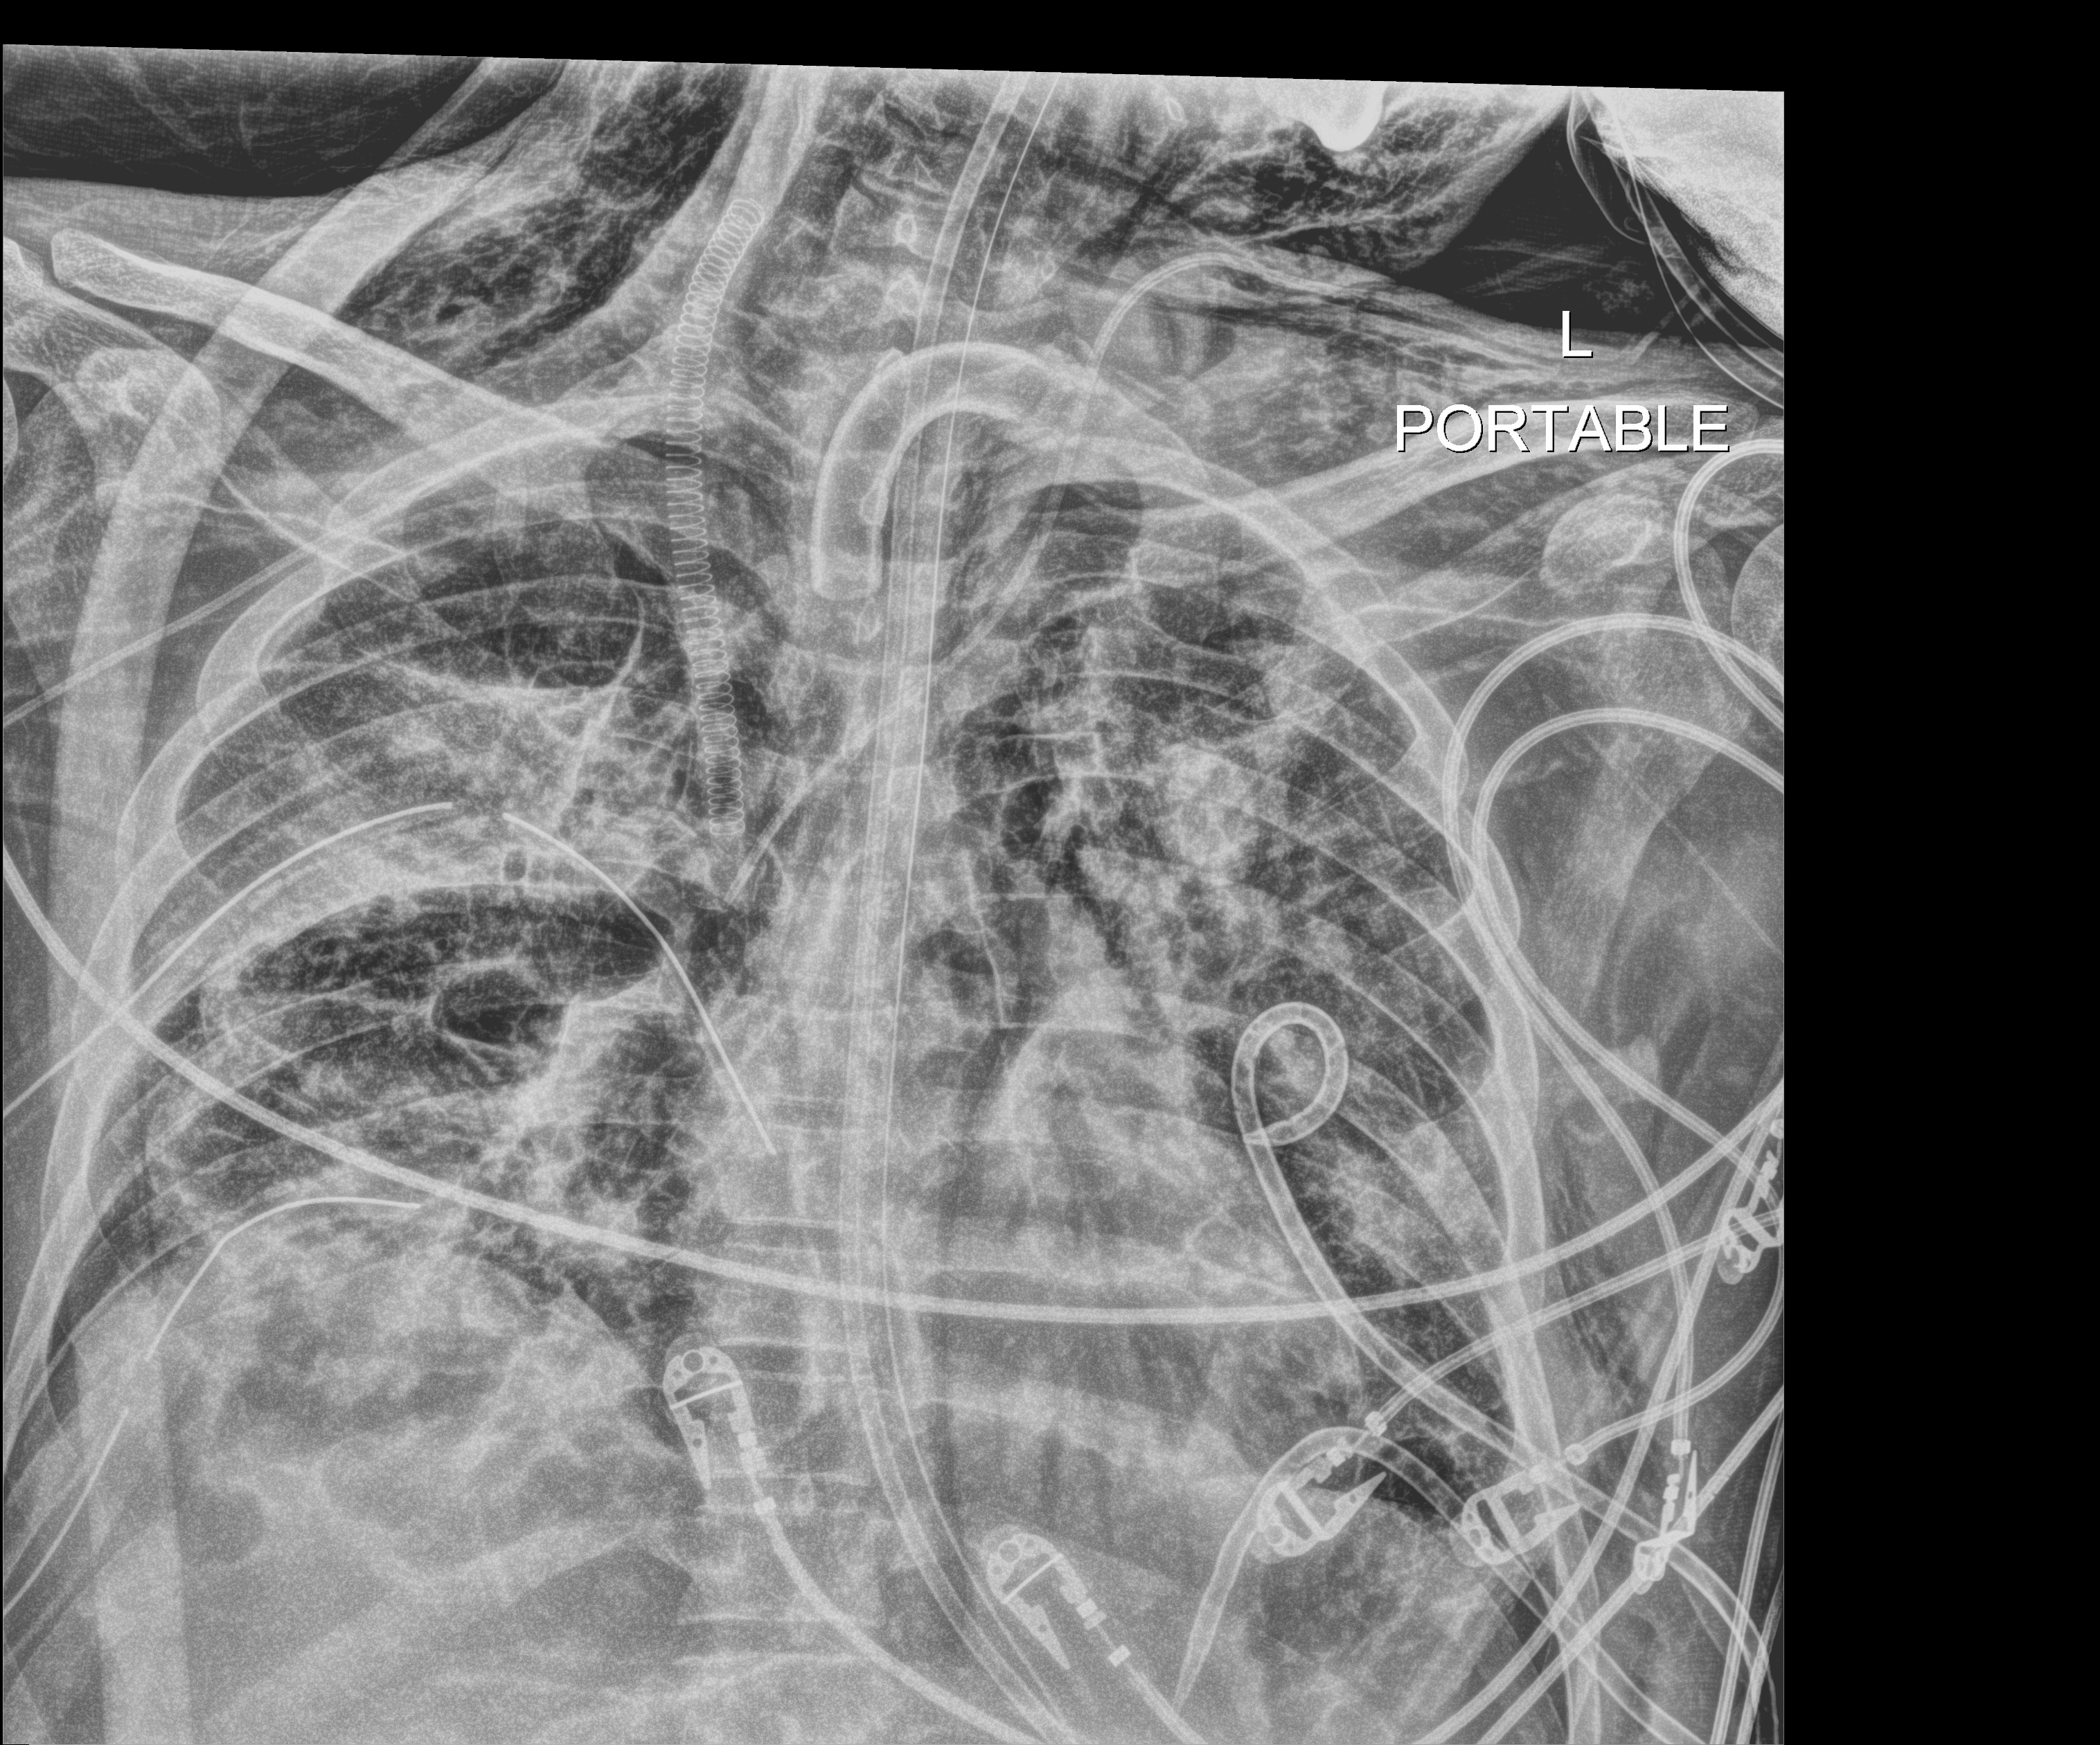
Chest X-ray; anteroposterior (AP) projection. Patient hospitalised with COVID-19, aged 18–59 years.
Admission-level facts for this patient (not findings on this image; timing relative to this image not recorded): COPD (admission record): no; mechanically ventilated during this hospital stay: yes.